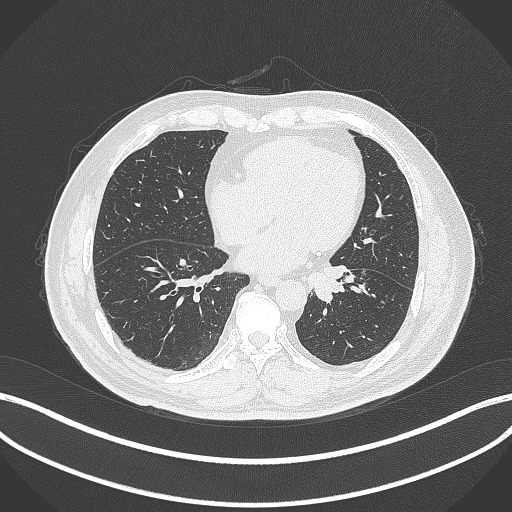
Chest CT, one axial slice; slice 99 of 312 in the series (ordered by position); 120 kVp; lung window (W 1500 / L -600 HU); 1 mm slice thickness; 512 × 512 image matrix, field of view 400 × 400 mm. Patient: male, 71 years. From the clinical record (not read from this slice): clinical TNM (as recorded): T1b N0 M0.
Annotated regions visible in this slice (rectangle marked by the reading radiologist):
- lung tumour (recorded histology: squamous cell carcinoma): bounding box (x1, y1, x2, y2) in pixels: (309, 264, 350, 301)